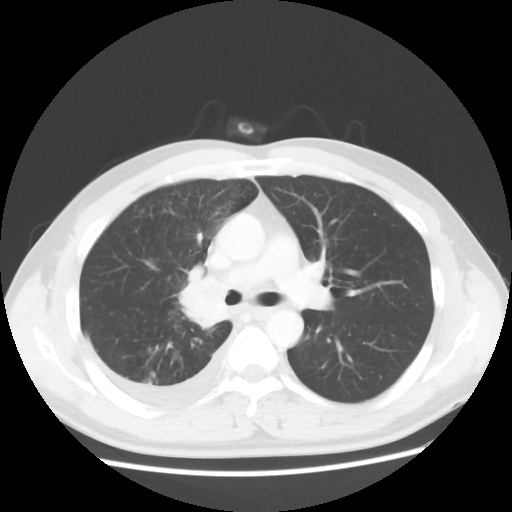
Chest CT, one axial slice. Position 34 of 56 along the scan axis. 120 kVp. Lung window (W 1500 / L -600 HU). 5 mm slice thickness. 512 × 512 image matrix, field of view 360 × 360 mm. Male patient, age 46 years. Case-level facts recorded for this patient, not image findings: clinical TNM (as recorded): T2 N3 M1.
Annotated regions visible in this slice (bounding box drawn by a radiologist):
- lung tumour (recorded histology: adenocarcinoma): bounding box <178,275,227,329> (left, top, right, bottom; pixels)